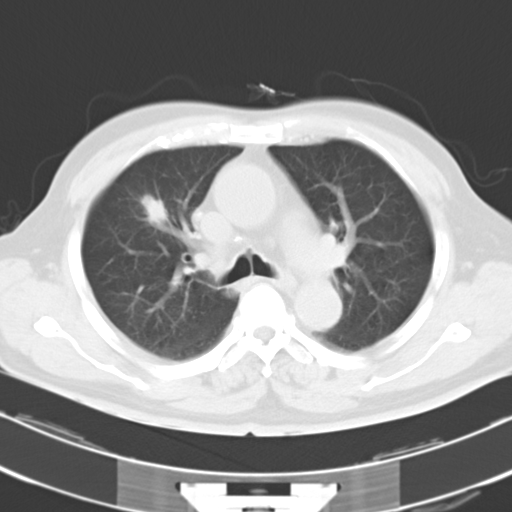
Chest CT, one axial slice. Position 19 of 29 along the scan axis. 120 kVp. Lung window (W 1500 / L -600 HU). 10 mm slice thickness. 512 × 512 image matrix. Male patient, age 70 years. From the clinical record (not read from this slice): clinical TNM (as recorded): T1b N0 M0.
Structures marked on this image (bounding box drawn by a radiologist):
- lung tumour (recorded histology: adenocarcinoma): bounding box <142,194,169,230> (left, top, right, bottom; pixels)